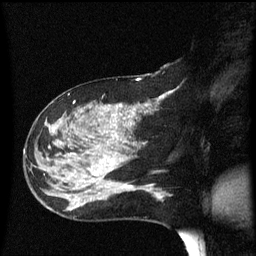
Breast MRI (dynamic contrast-enhanced), one sagittal slice. Slice 28 of 60 in the series (ordered by position). Dynamic contrast-enhanced series, image 2 of 3 at this slice position (ordered by acquisition). 1.5 T. TE 4.2 ms, TR 8.4 ms. 2.2 mm slice thickness. 256 × 256 image matrix, field of view 200 × 200 mm. Patient: female, 47 years.
Annotated regions visible in this slice (semi-automatic segmentation, software-assisted and operator-edited):
- analysis volume of interest (the breast-tissue region the enhancement analysis was run in; not a lesion): bounding box (x1, y1, x2, y2) in pixels: (24, 97, 149, 206)
- tumour enhancement mask (voxels above the 70 % enhancement threshold inside the analysis volume of interest): (82, 106, 147, 188)